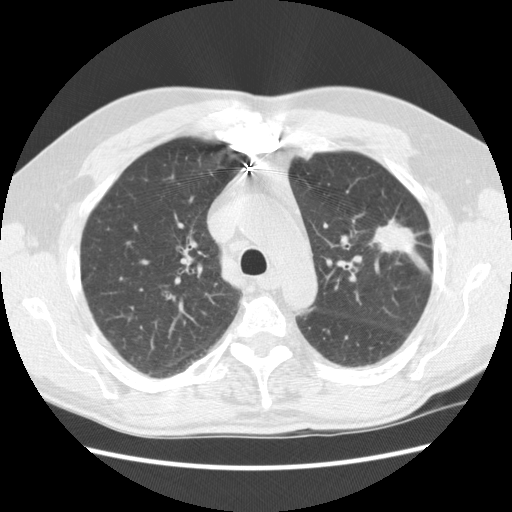
Low-dose screening chest CT, one axial slice. Slice 171 of 231 in the series (ordered by position). Reconstruction kernel STANDARD. 120 kVp. Lung window (W 1500 / L -600 HU). 512 × 512 image matrix, field of view 362 × 362 mm.
Structures marked on this image (expert manual segmentation):
- lesion 1 (tumor, upper lobe of left lung): bounding box (x1, y1, x2, y2) in pixels: (372, 219, 417, 253)